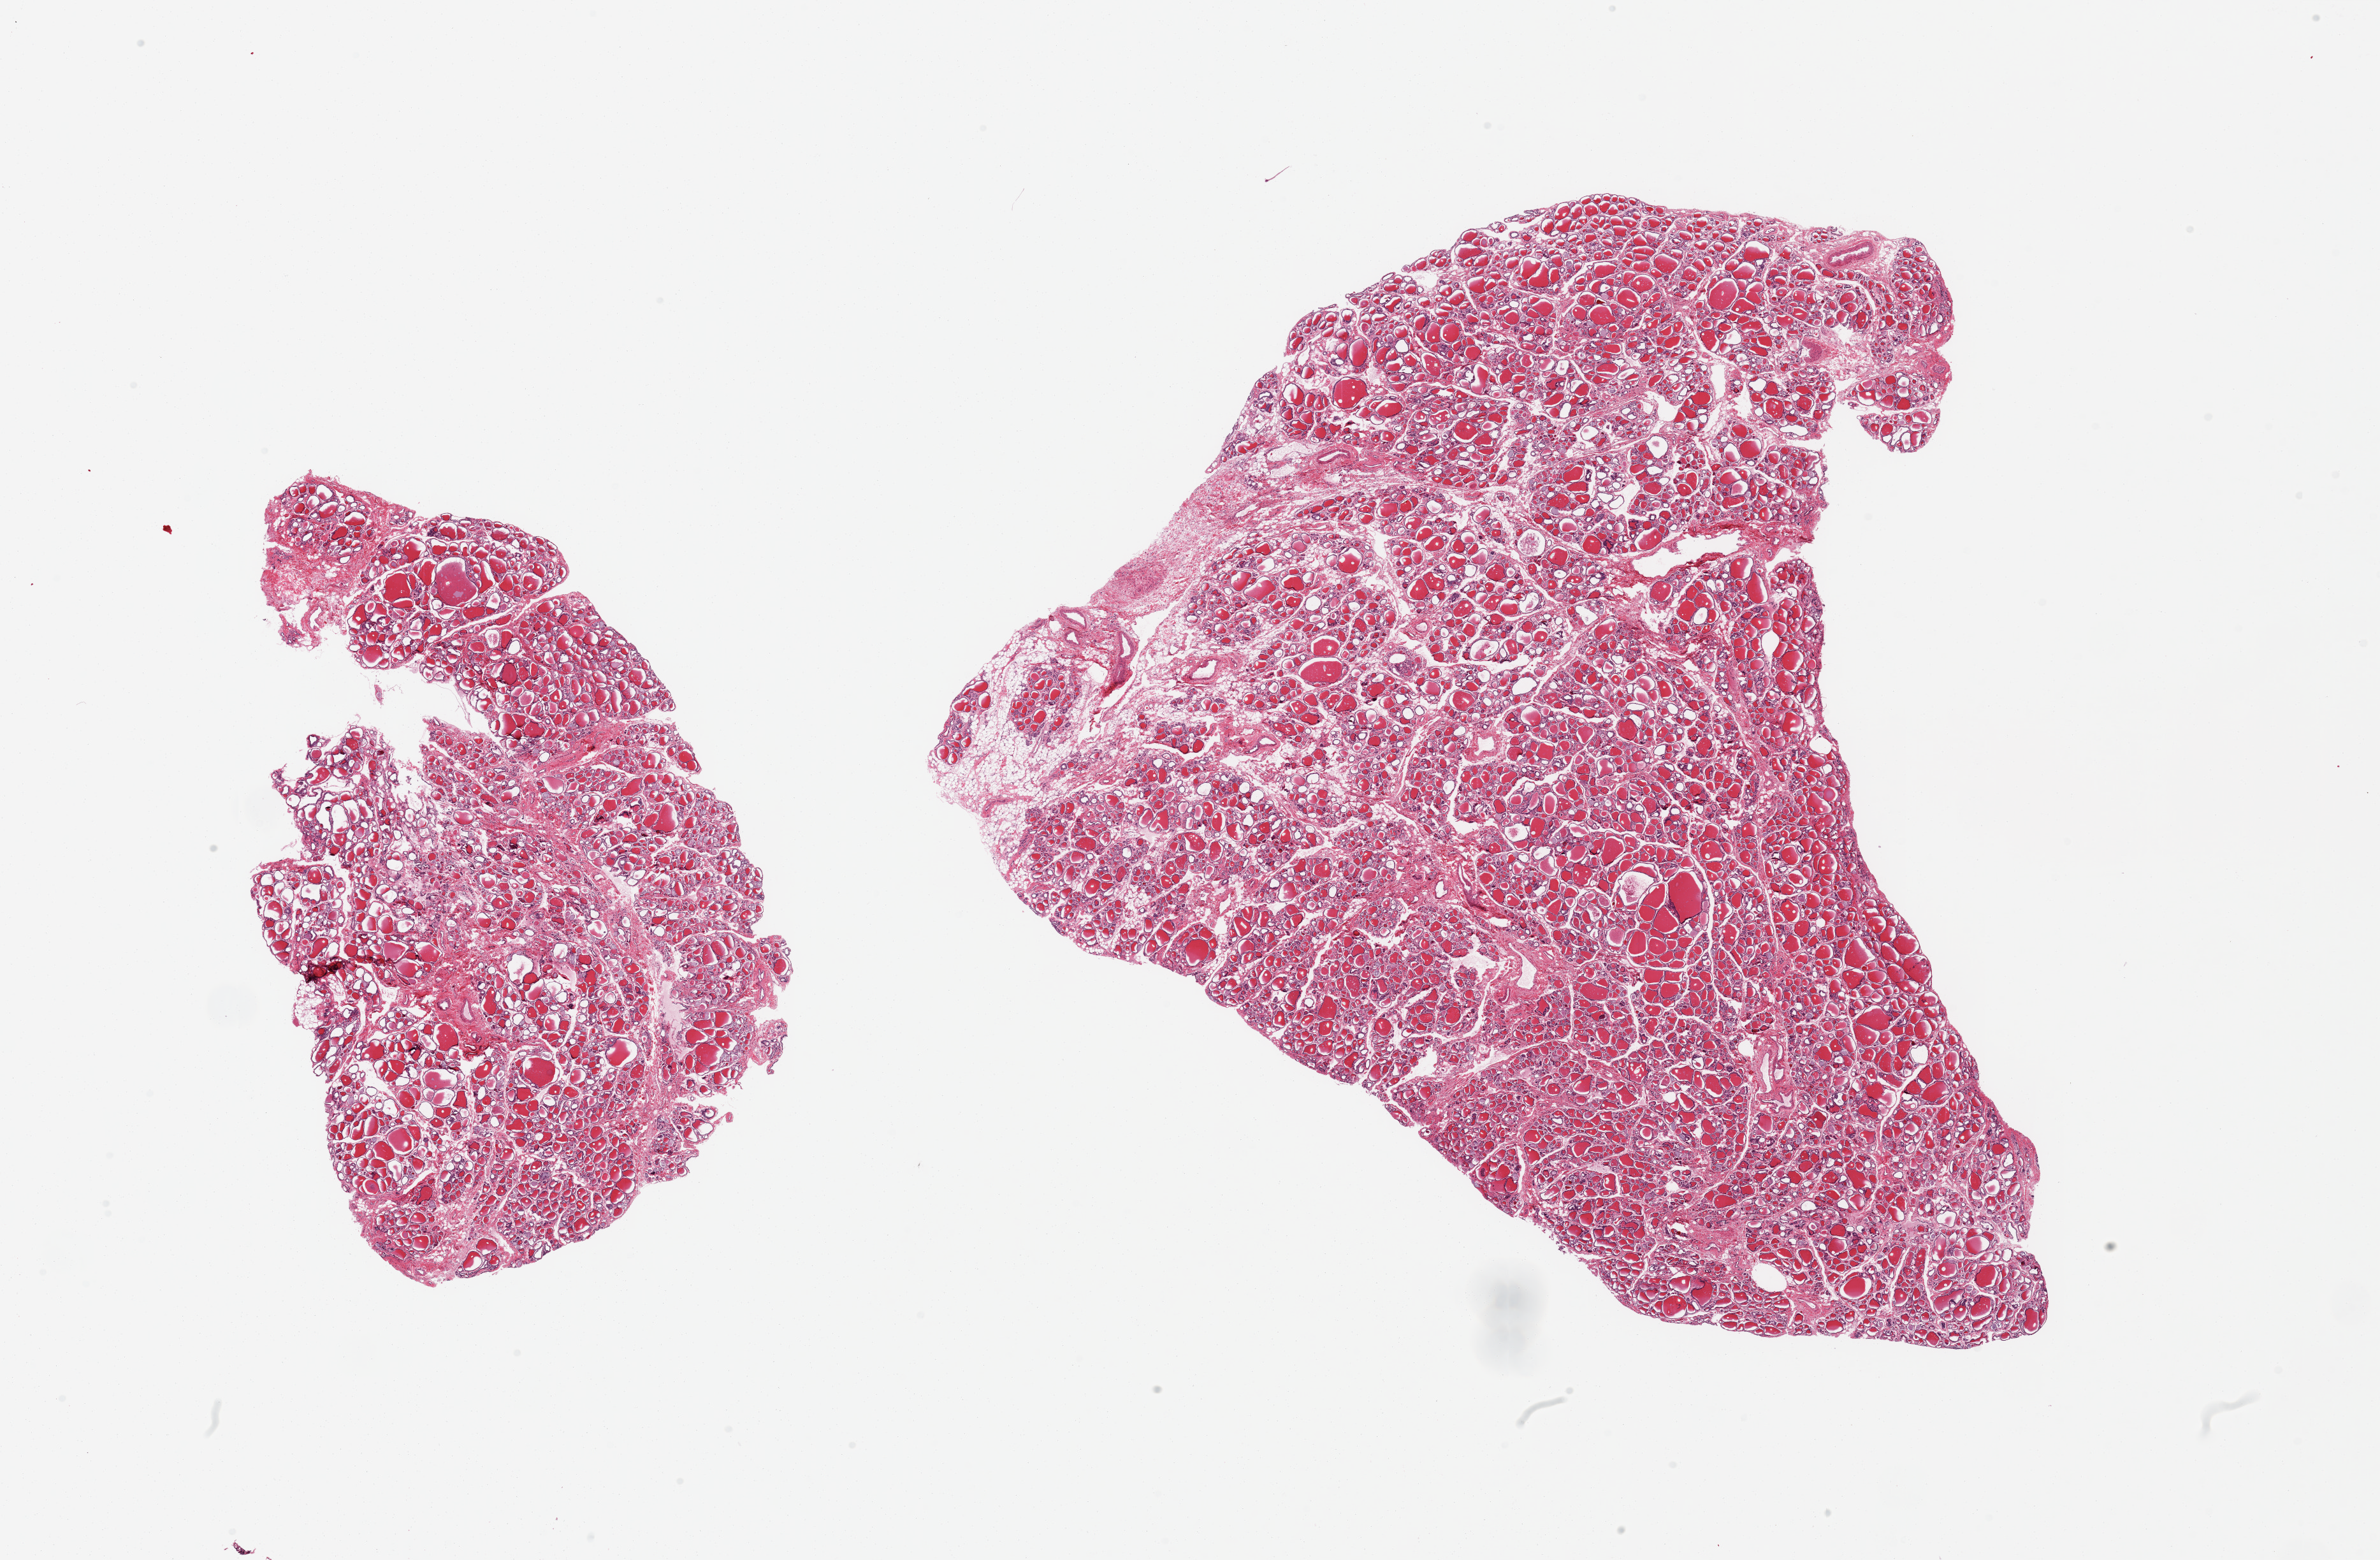
Whole-slide image, hematoxylin and eosin (H&E) stain, a low-resolution overview of the entire scanned area, about 29.5 x 19.4 mm (from a 20x scan); PAXgene-fixed, paraffin-embedded tissue; sampled site (target tissue): thyroid; donor tissue sample. Donor: male.
• review note (as recorded): 2 pieces, no abnormalities